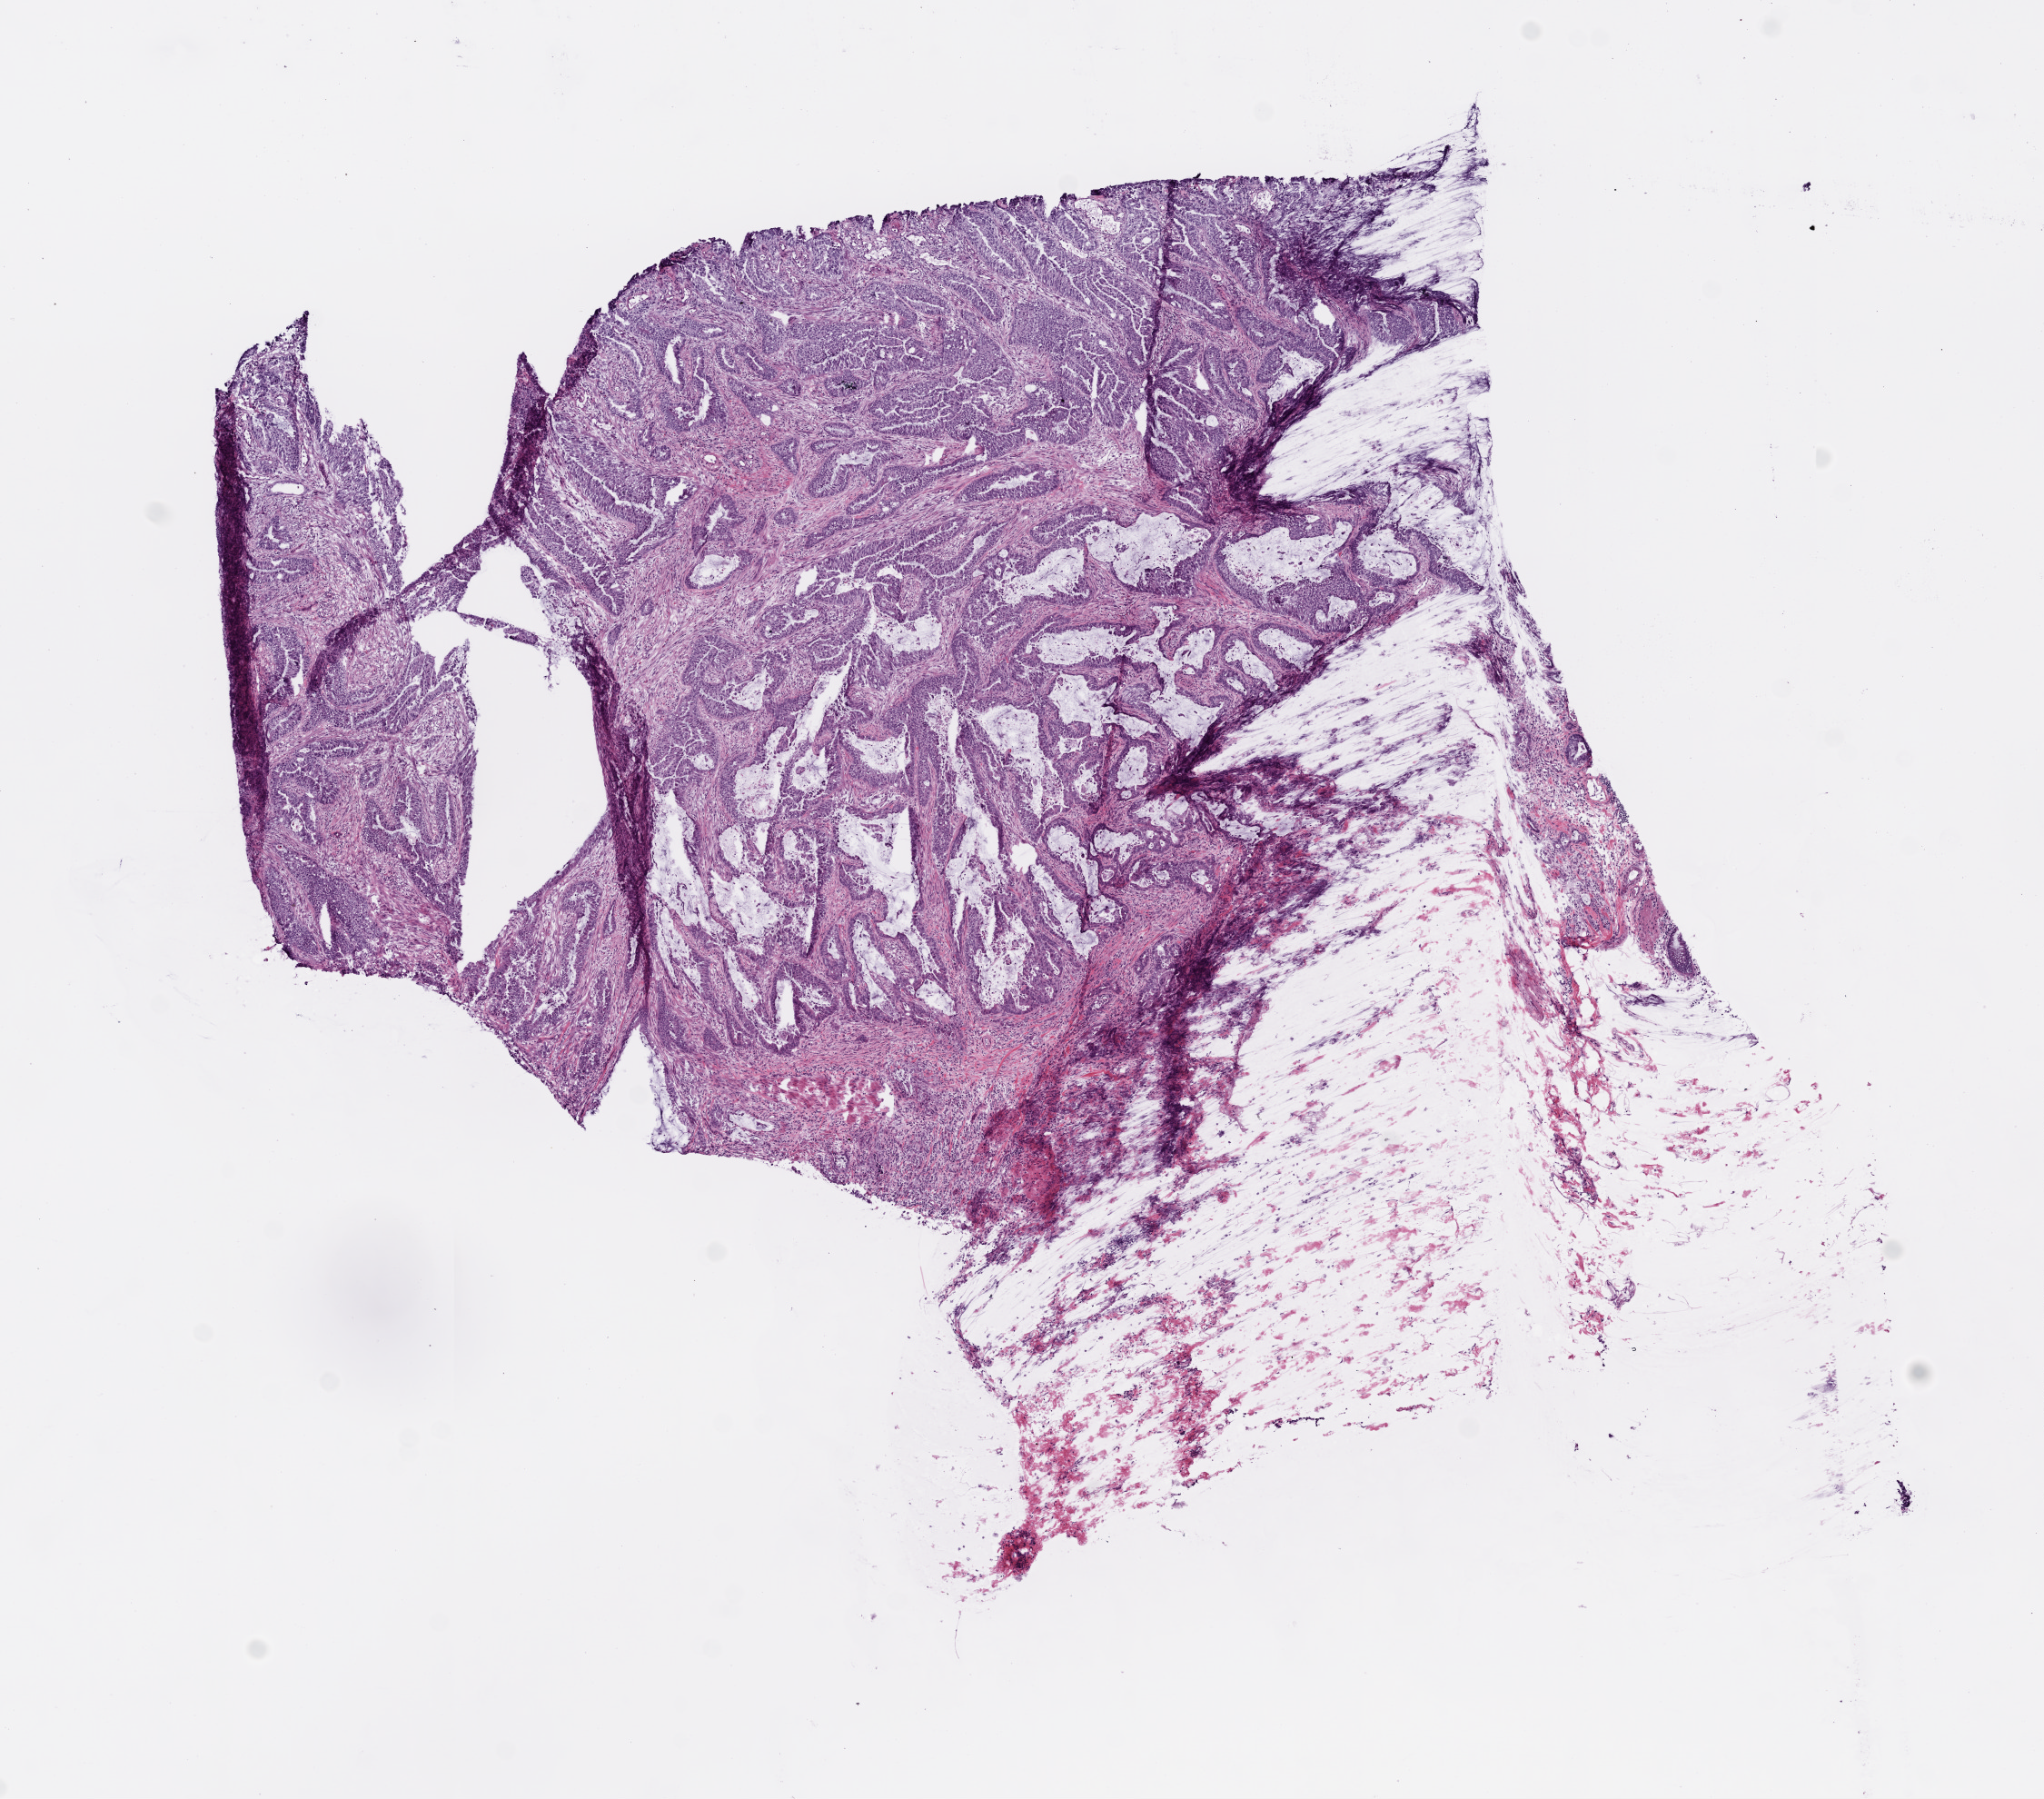
Digitized Hematoxylin and eosin (H&E) stained tissue section (whole slide) — low-resolution overview of the scanned area, about 9.0 x 7.9 mm; frozen section from the top of the tissue portion; sample: primary tumour, colon. Patient: male, age at initial diagnosis 60 years. Slide review estimates, as recorded: tumour cells 90%, tumour nuclei 80%, normal cells 0%, stromal cells 10%, necrosis 0%. Inflammatory infiltration, as recorded: lymphocyte infiltration 11%, monocyte infiltration 0%, neutrophil infiltration 2%.
* AJCC pathologic stage: IIIA
* pathologic diagnosis: Mucinous adenocarcinoma (ascending colon)
* TNM: T3 N1 M0